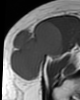
MRI of an extremity soft-tissue mass, one axial slice; position 22 of 46 along the scan axis; MR volume resampled by the dataset authors to the PET/CT grid (not the native acquisition matrix); 3.27 mm slice thickness; 80 × 100 image matrix. Female patient. From the clinical record (not read from this slice): histological type: synovial sarcoma; grade: intermediate; site of the primary tumour: right thigh.
Structures marked on this image (expert contour drawn on MRI and transferred to this co-registered scan by the dataset authors):
- gross tumour volume including surrounding oedema: bounding box <10,21,65,82> (left, top, right, bottom; pixels)
- gross tumour volume (mass): <10,21,65,82>